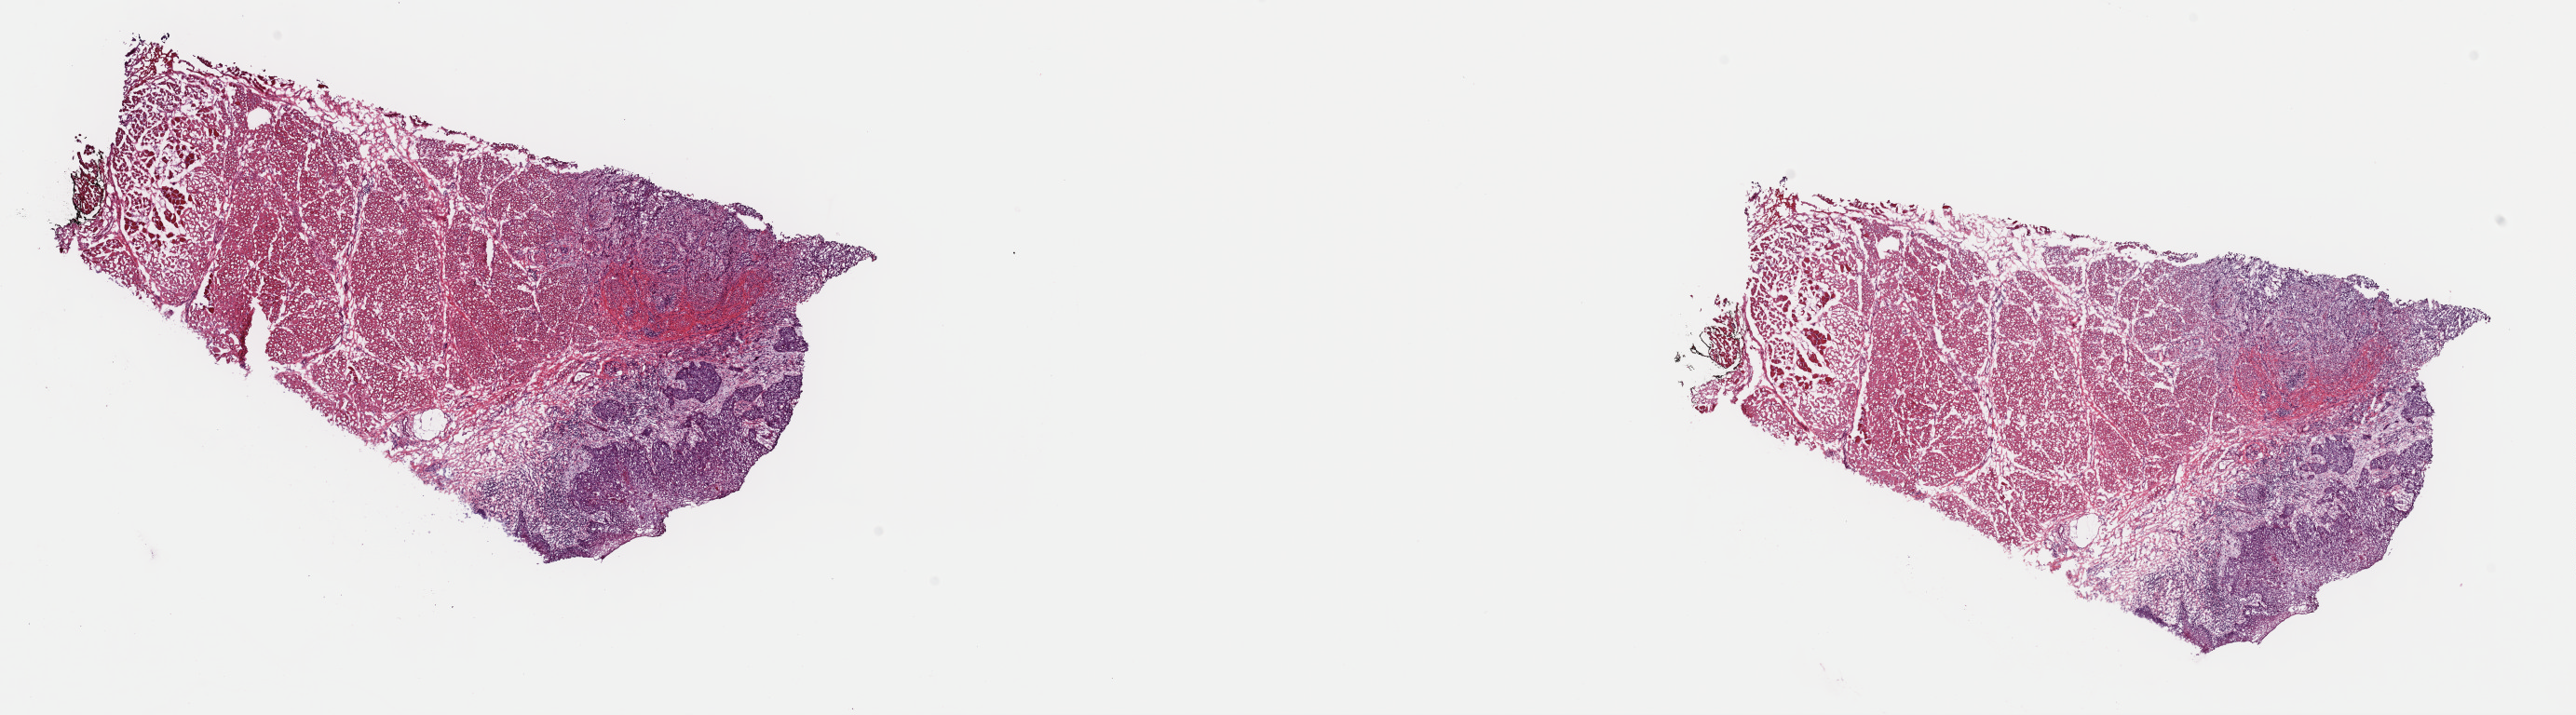
H&E-stained whole-slide image, a low-resolution overview of the entire scanned area, about 21.9 x 6.1 mm, frozen section from the top of the tissue portion, primary tumour sample from the head and neck. Male, age 41 years at initial diagnosis. Histologic grade: G3 (poorly differentiated). Composition of this section per pathologist review: tumour cells 22%, tumour nuclei 60%, normal cells 58%, stromal cells 15%, necrosis 5%. Infiltration values recorded for this section: lymphocyte infiltration 8%, monocyte infiltration 4%, neutrophil infiltration 2%.
Lymph nodes positive (case pathology): 2 of 16 examined. Laterality: right. TNM: T2 N2b M0. AJCC pathologic stage: IVA. Pathologic diagnosis: Squamous cell carcinoma, NOS (tongue, NOS).